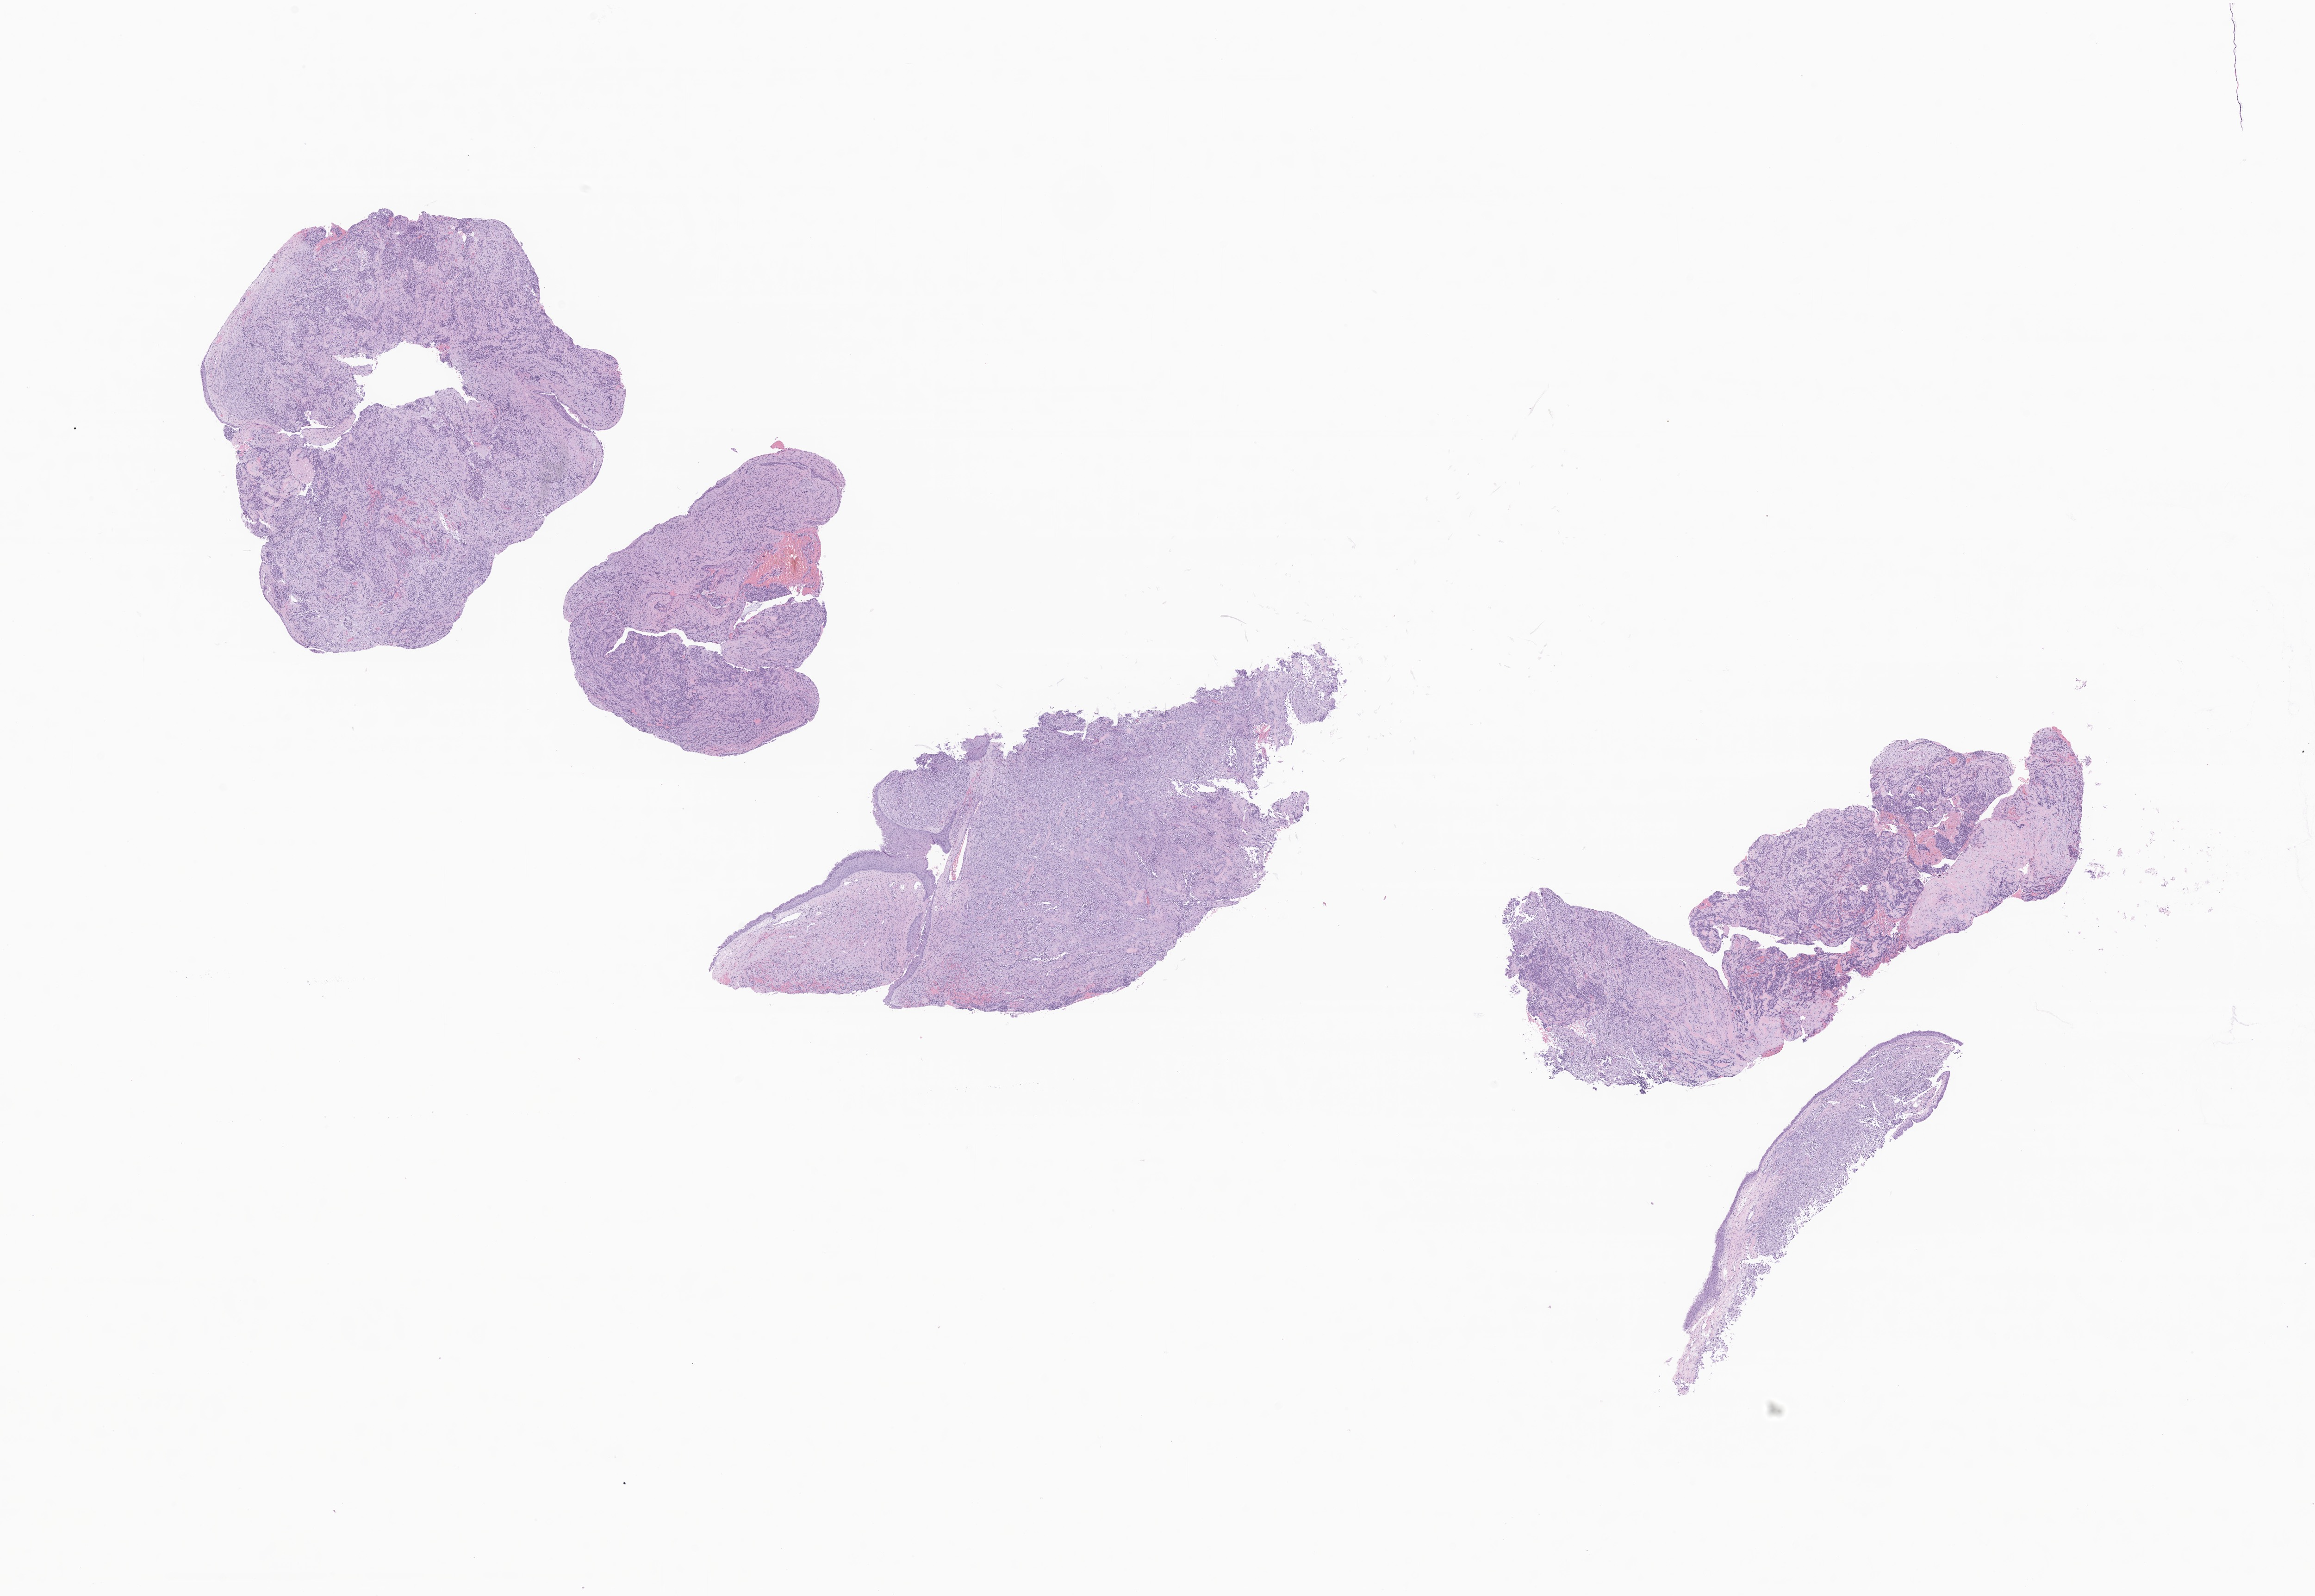
Hematoxylin and eosin (H&E) whole-slide image of tumor tissue from the nasal cavity — low-resolution overview of the scanned area, about 21.1 x 14.5 mm, formalin-fixed paraffin-embedded section. Patient male; age 274 days.
• diagnosis: Embryonal rhabdomyosarcoma, NOS